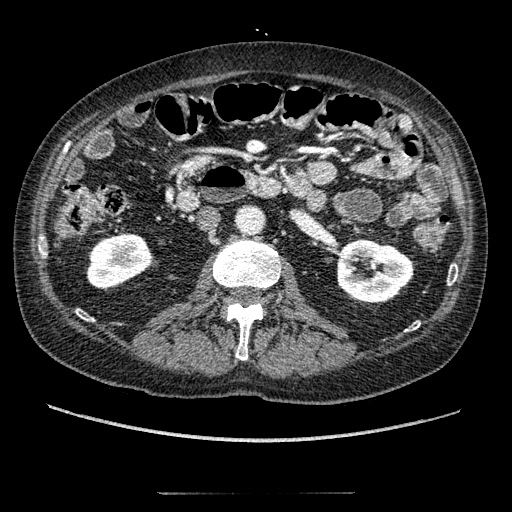
Contrast-enhanced abdominal CT, one axial slice. Reconstruction kernel STANDARD. 120 kVp. Intravenous contrast given. Soft-tissue window (W 400 / L 40 HU). 512 × 512 image matrix, field of view 381 × 381 mm. Patient: male, 69 years. From the clinical record (not read from this slice): diagnosis: adrenocortical carcinoma; tumour side: left adrenal; tumour size at pathology: 6.1 cm; Ki-67 index: 10 %; stage (as recorded): 3.
Outlined on this slice (semi-automatic segmentation, software-assisted and operator-edited):
- mass: box from (x=308, y=191) to (x=326, y=211) px